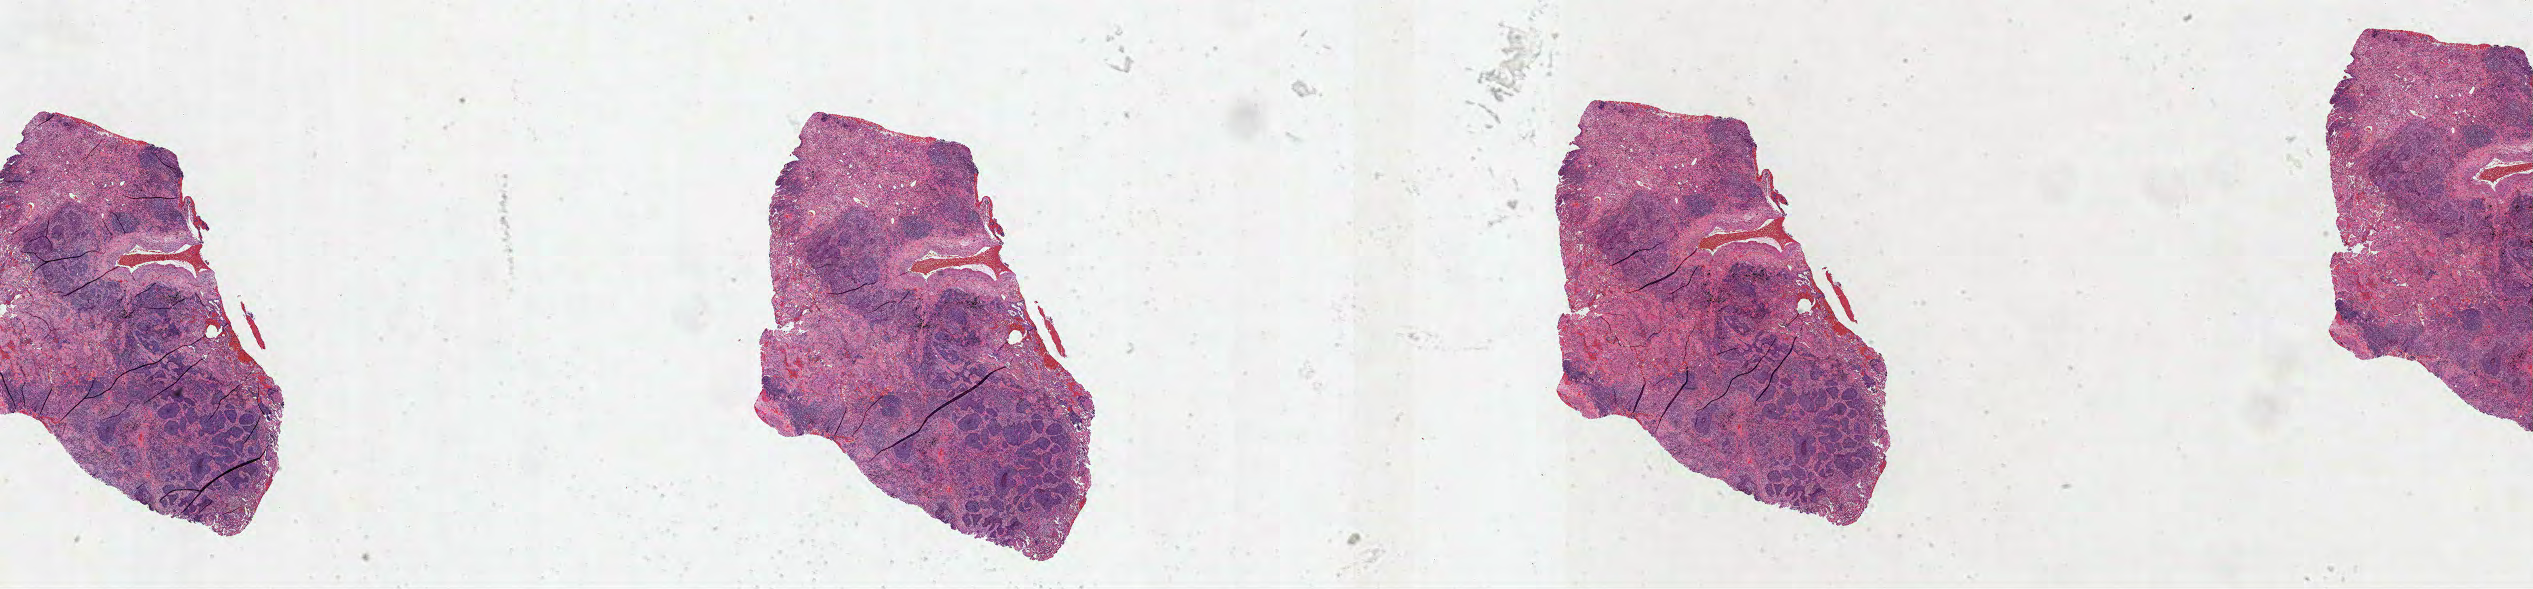
Digitized H&E-stained tissue section (whole slide) — a low-resolution overview of the entire scanned area, about 40.9 x 9.5 mm. FFPE section. Primary tumour sample from the lung. Male patient; age at initial diagnosis 71 years.
AJCC pathologic stage: IA (7th edition). Histologic diagnosis: Squamous cell carcinoma, NOS. TNM: T1b N0 MX.